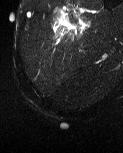
MRI of an extremity soft-tissue mass, one axial slice; slice 7 of 60 in the series (ordered by position); T2-weighted fat-saturated; MR volume resampled by the dataset authors to the PET/CT grid (not the native acquisition matrix); 3.27 mm slice thickness; 123 × 153 image matrix. Male patient. Case-level facts recorded for this patient, not image findings: histological type: pleiomorphic liposarcoma; grade: high; site of the primary tumour: left thigh.
Outlined on this slice (expert contour drawn on MRI and transferred to this co-registered scan by the dataset authors):
- gross tumour volume including surrounding oedema: bounding box <52,11,91,37> (left, top, right, bottom; pixels)